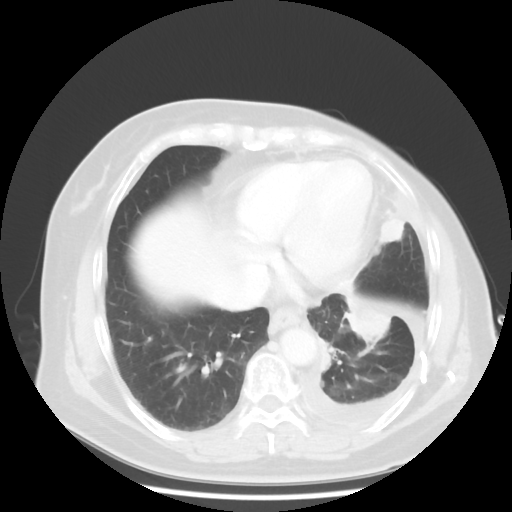
Chest CT, one axial slice; lung window (W 1500 / L -600 HU); 512 × 512 image matrix, field of view 360 × 360 mm. Female patient, age 63 years. From the clinical record (not read from this slice): clinical TNM (as recorded): T2 N0 M1.
Outlined on this slice (rectangle marked by the reading radiologist):
- lung tumour (recorded histology: adenocarcinoma): bounding box <332,292,392,355> (left, top, right, bottom; pixels)